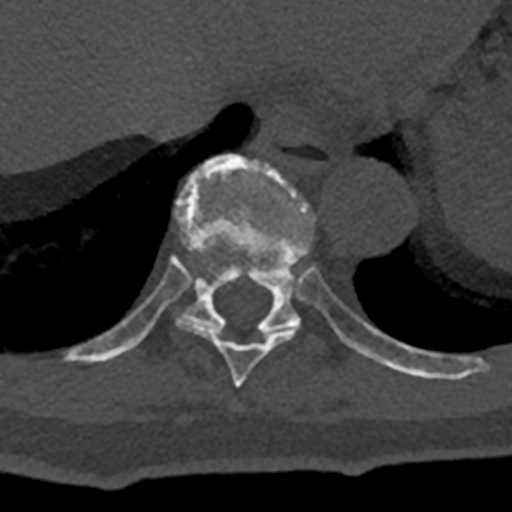
CT including the spine, one axial slice; reconstruction kernel Br40s/3; 120 kVp; bone window (W 1800 / L 400 HU); 512 × 512 image matrix. Patient: male, 74 years. Case-level facts recorded for this patient, not image findings: primary cancer: renal; vertebrae with lytic lesions (as recorded): T10, L1, L2, L3, L4, L5.
Outlined on this slice (semi-automatically segmented with operator editing):
- T10 vertebra: bounding box (x1, y1, x2, y2) in pixels: (70, 154, 432, 379)
- T9 vertebra: (176, 317, 296, 388)